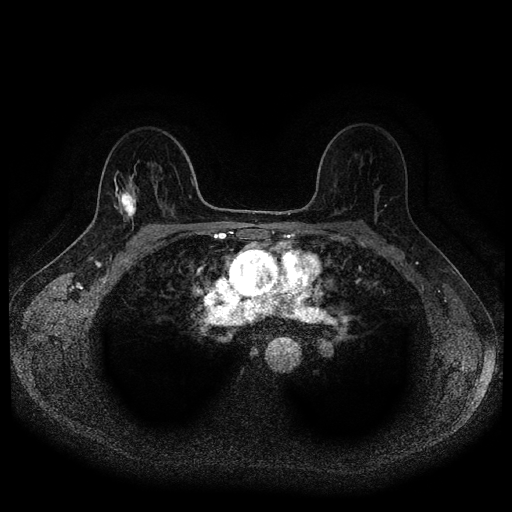
Breast MRI (dynamic contrast-enhanced, multi-phase), one axial slice. Slice 66 of 116 in the series (ordered by position). Dynamic contrast-enhanced series, time point 2 of 5 at this slice position (early post-contrast). 1.5 T. TE 2.6 ms, TR 5.4 ms. 2 mm slice thickness. 512 × 512 image matrix, field of view 340 × 340 mm. Patient: female, 49 years.
Structures marked on this image (semi-automatically segmented with operator editing):
- breast lesion (labelled 'tumour' in the annotation; benign lesions carry a separate 'benign' label): bounding box (x1, y1, x2, y2) in pixels: (116, 185, 137, 222)